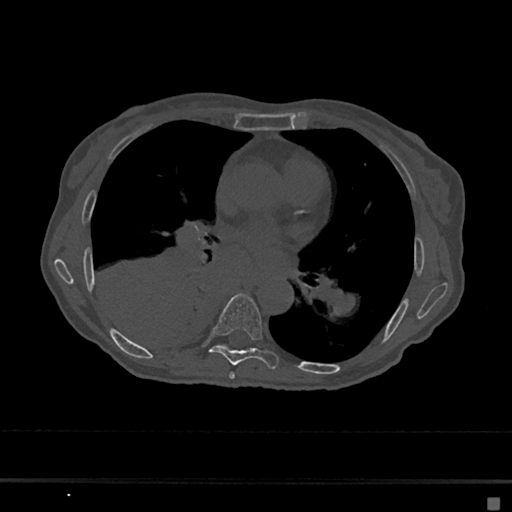
CT including the spine, one axial slice. Position 369 of 797 along the scan axis. Bone window (W 1800 / L 400 HU). 0.5 mm slice thickness. 512 × 512 image matrix. Female patient, age 68 years. Case-level facts recorded for this patient, not image findings: primary cancer: renal.
Outlined on this slice (semi-automatically segmented with operator editing):
- T6 vertebra: bounding box [x1, y1, x2, y2] px = [229, 372, 235, 379]
- T7 vertebra: [209, 294, 279, 370]